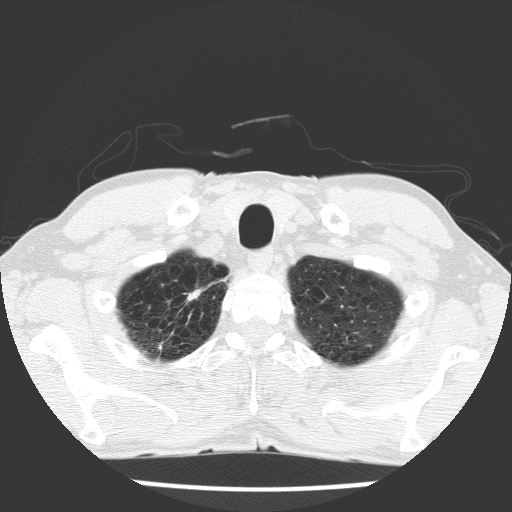
Low-dose screening chest CT, axial slice, baseline annual screen, lung window (W 1500 / L -600 HU), 2 mm slice thickness. Male, age 63 years at enrolment. Current smoker at enrolment.
• Lesion marked by an expert reader, bounding box [x1, y1, x2, y2] px = [154, 275, 220, 340].
• Screening reader's record for this exam: no non-calcified nodule ≥4 mm recorded.
• Official screen result: negative screen, significant abnormalities not suspicious for lung cancer.